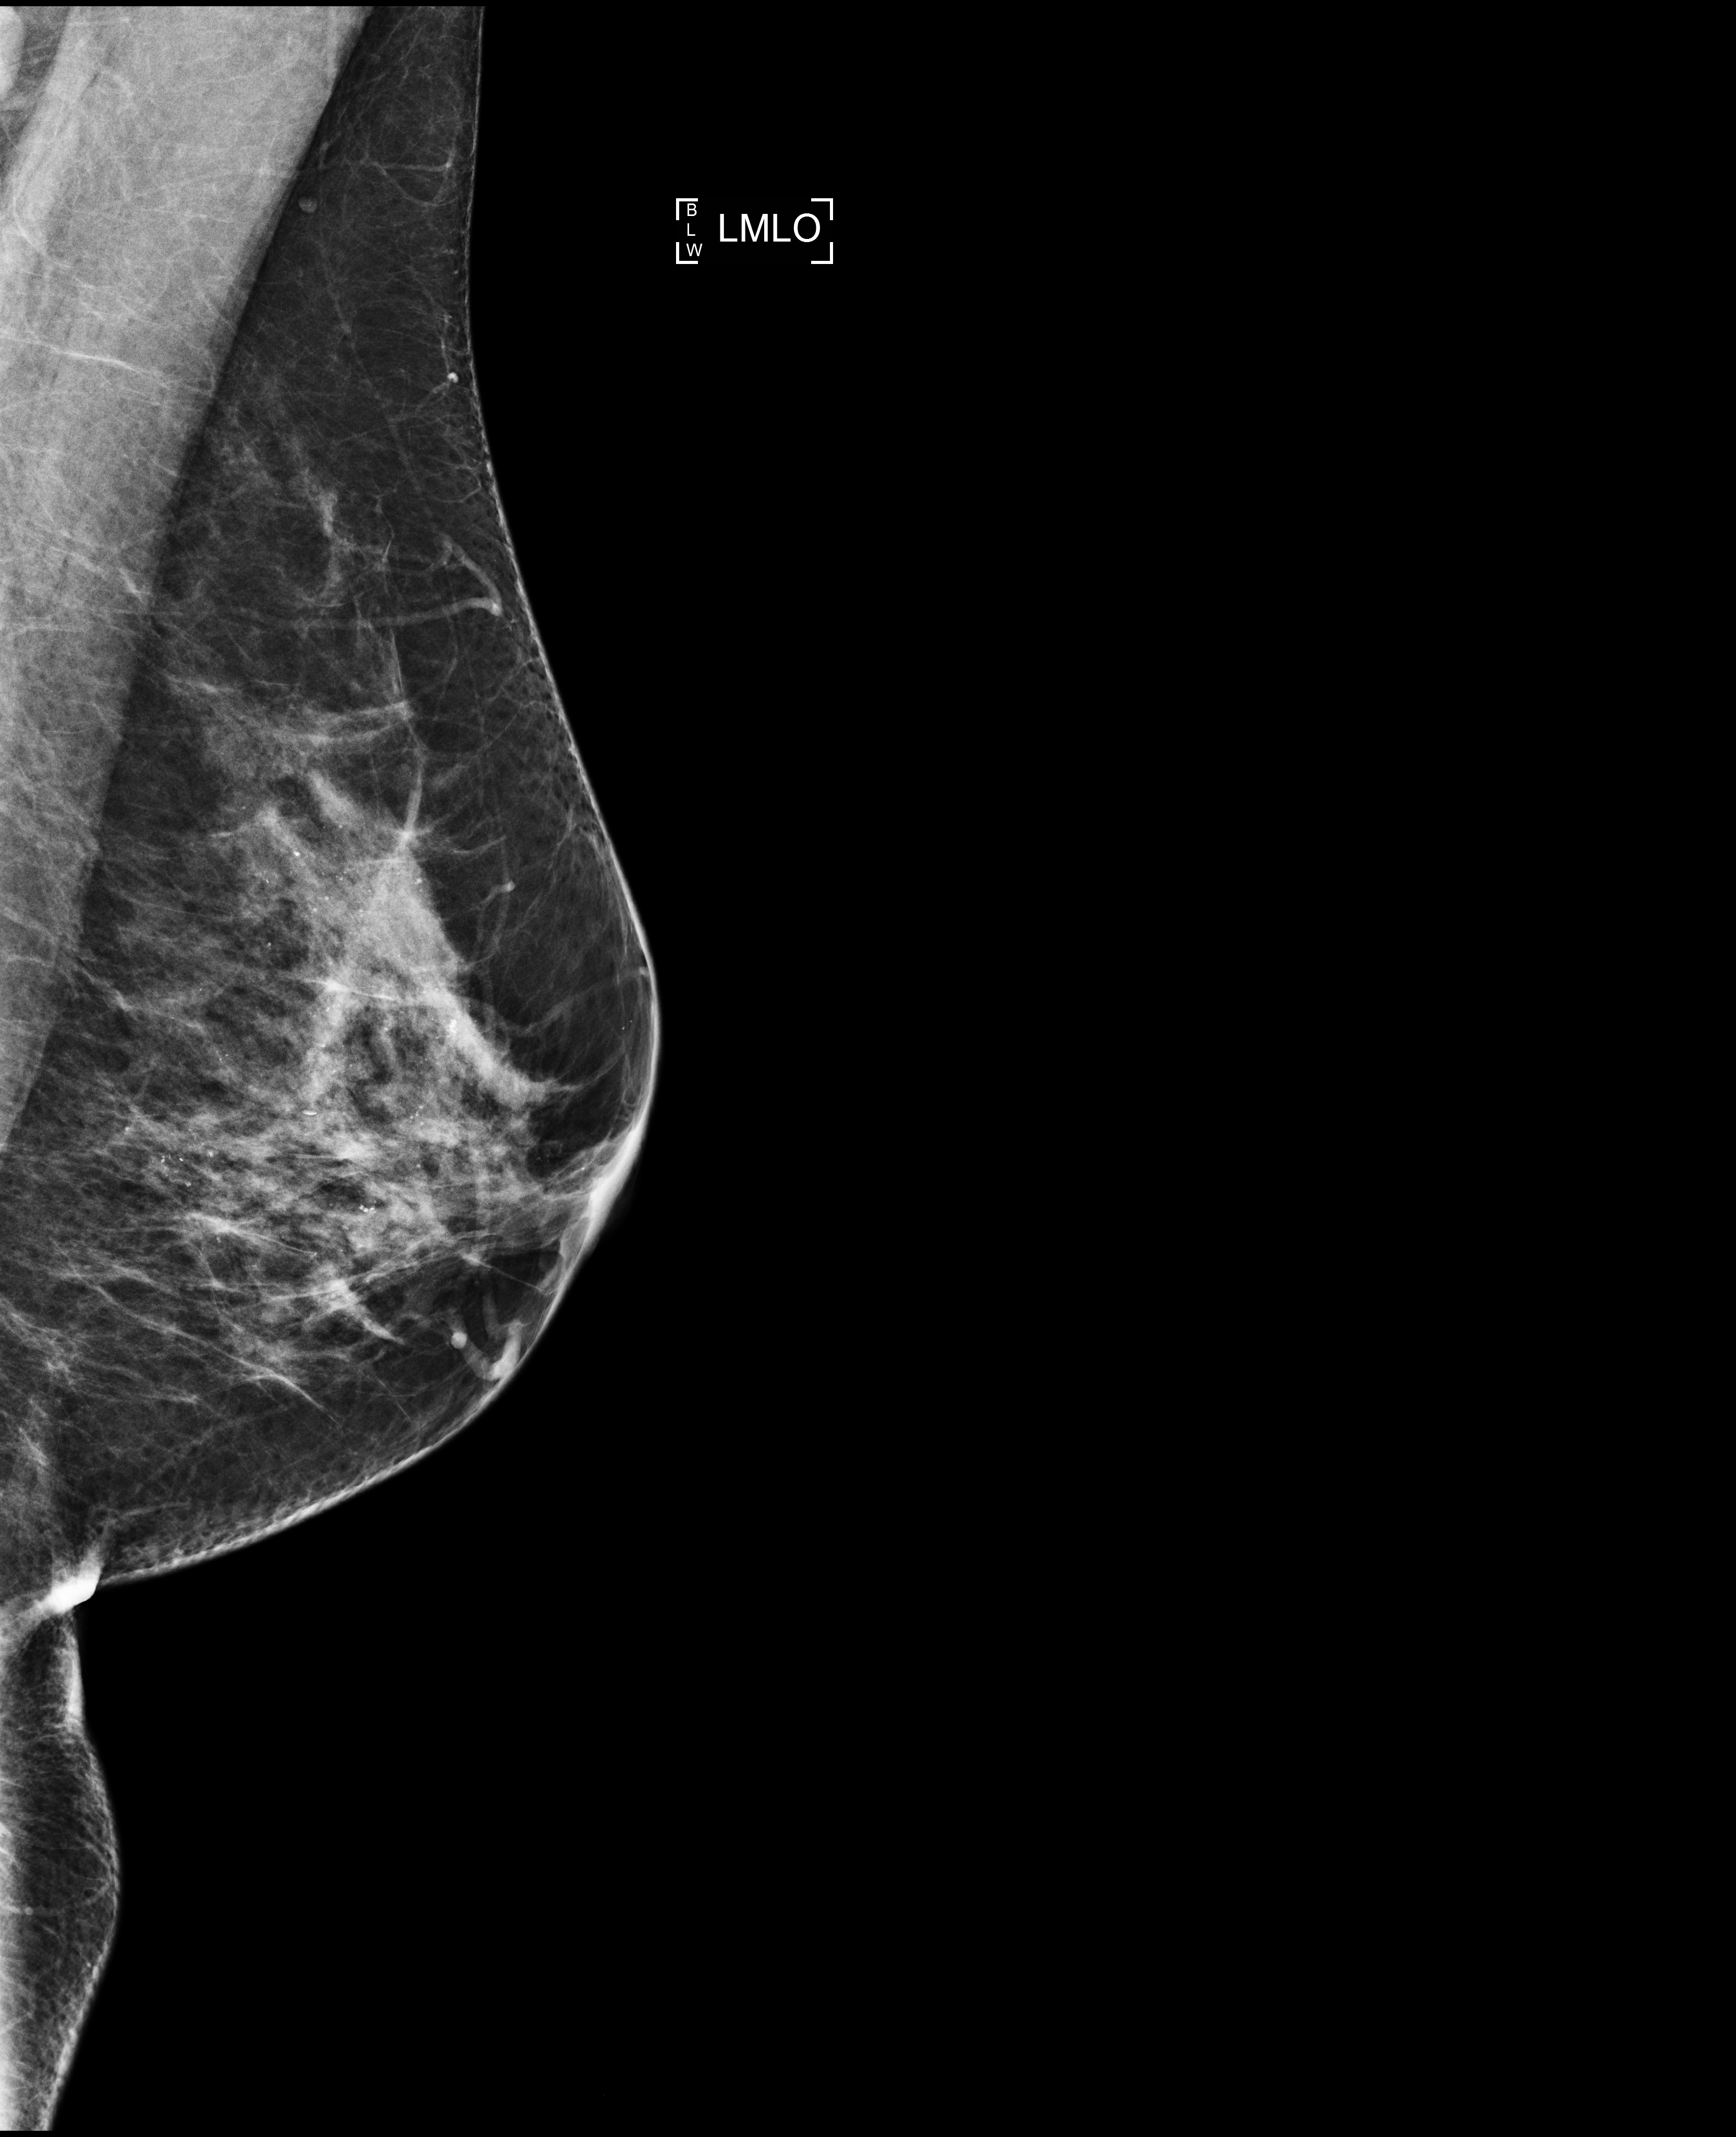
Annual screening mammography examination; system: Selenia Dimensions. Female patient, age 50 years.
Image type: full-field digital mammogram. Breast: left. Projection: medio-lateral oblique projection.